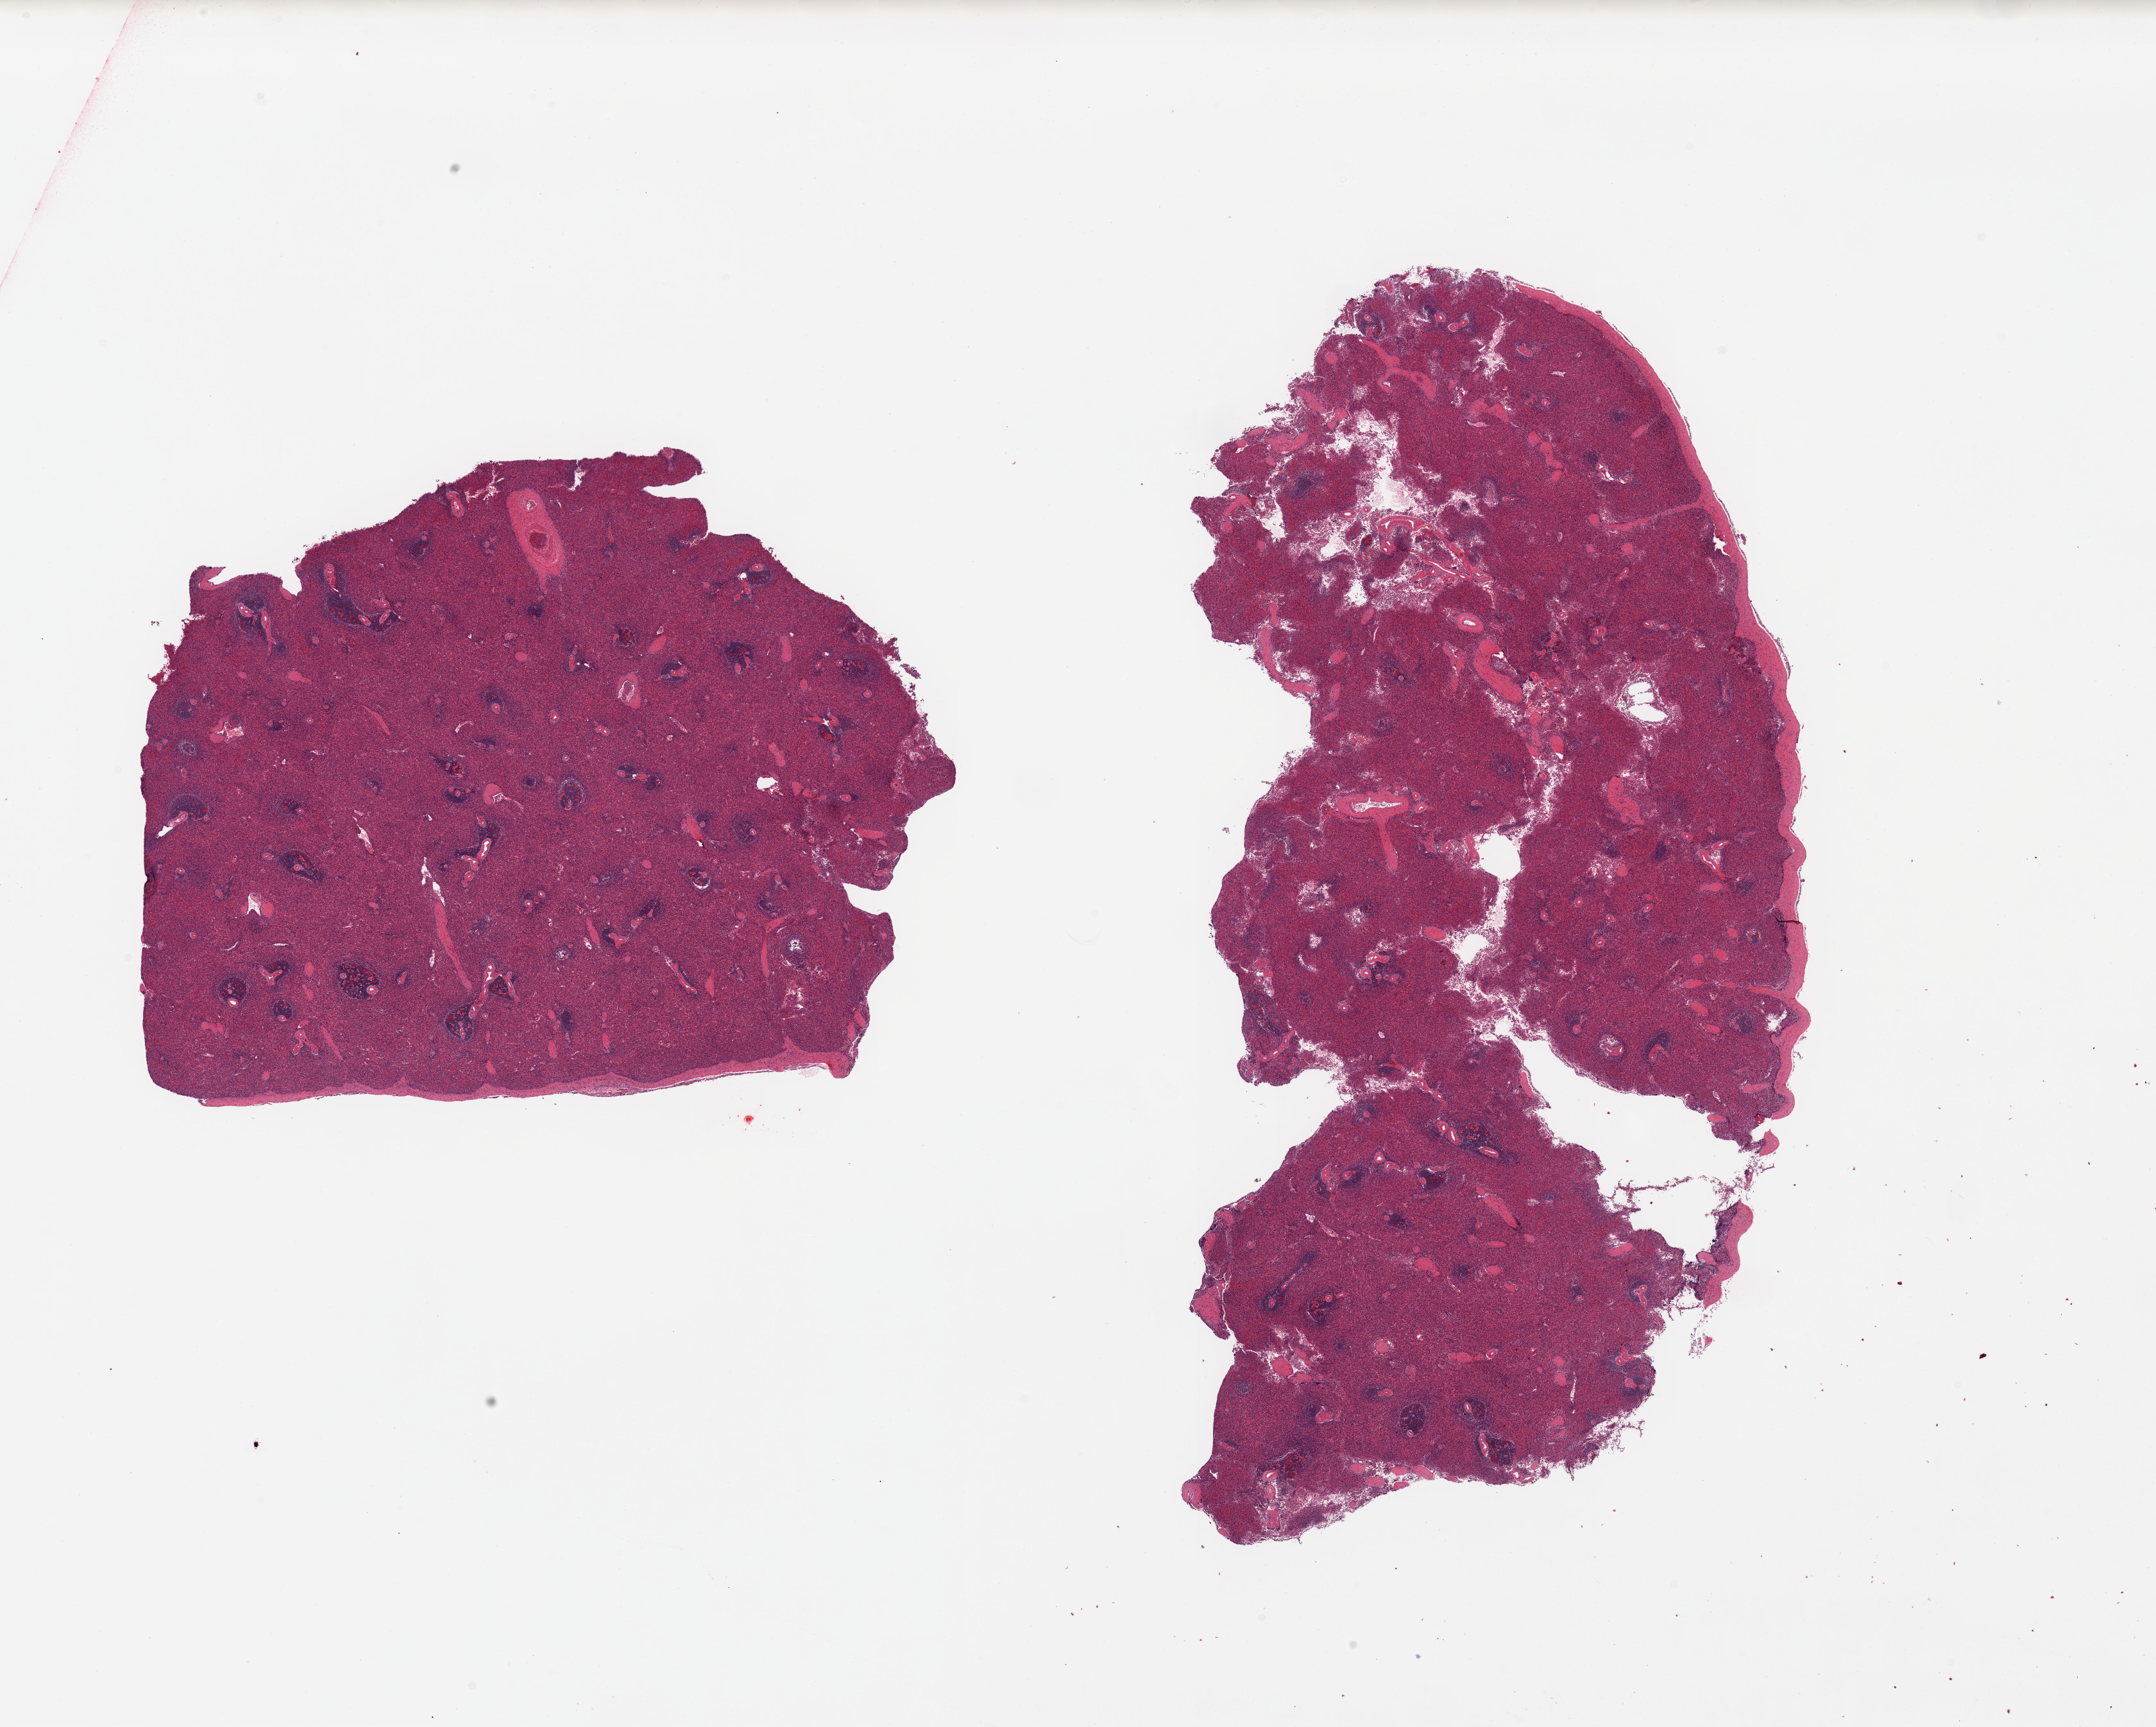
Digitized haematoxylin and eosin-stained section, brightfield, low-resolution overview of the scanned area, about 26.6 x 21.3 mm (acquisition: 20x scan); PAXgene-fixed paraffin-embedded (PFPE) section; target tissue: spleen; tissue donor sample. Donor: female.
Pathologist's review note for this sample: 2 pieces; capsule present on one side of each piece; not abnormally congested.